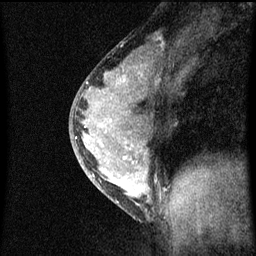
Breast MRI (dynamic contrast-enhanced), one sagittal slice; dynamic contrast-enhanced series, image 2 of 3 at this slice position (ordered by acquisition); 1.5 T; TE 4.2 ms, TR 8 ms; 2 mm slice thickness; 256 × 256 image matrix, field of view 180 × 180 mm. Patient: female, 33 years.
Annotated regions visible in this slice (semi-automatic segmentation, software-assisted and operator-edited):
- analysis volume of interest (the breast-tissue region the enhancement analysis was run in; not a lesion): bounding box [x1, y1, x2, y2] px = [70, 56, 164, 215]
- tumour enhancement mask (voxels above the 70 % enhancement threshold inside the analysis volume of interest): [77, 76, 151, 205]